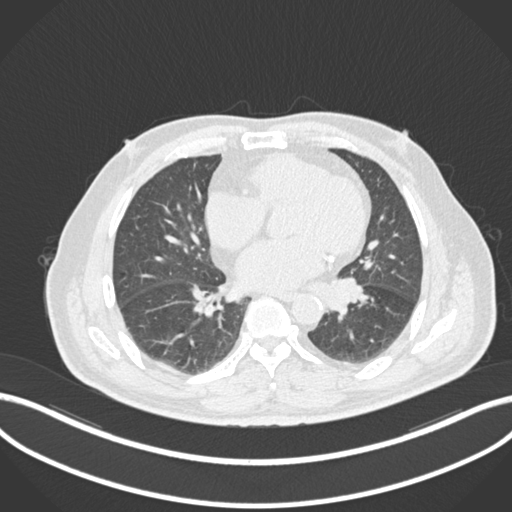
Chest CT, one axial slice. Position 54 of 161 along the scan axis. Reconstruction kernel B30f. Lung window (W 1500 / L -600 HU). 512 × 512 image matrix. Male patient, age 71 years. Case-level facts recorded for this patient, not image findings: clinical TNM (as recorded): T1b N0 M0.
Structures marked on this image (rectangle marked by the reading radiologist):
- lung tumour (recorded histology: squamous cell carcinoma): box from (x=325, y=276) to (x=367, y=313) px